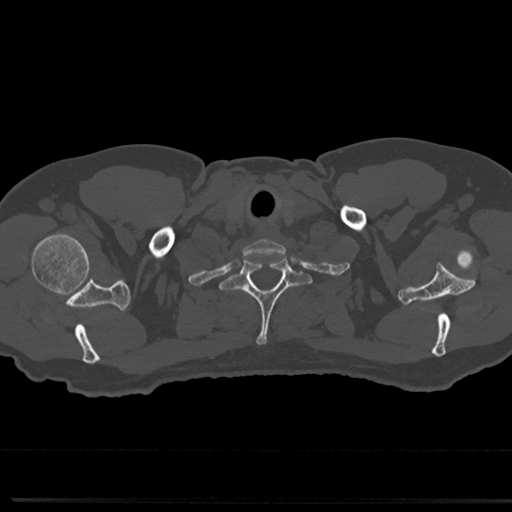
CT including the spine, one axial slice; slice 678 of 817 in the series (ordered by position); reconstruction kernel Br40s/3; 120 kVp; bone window (W 1800 / L 400 HU); 0.5 mm slice thickness; 512 × 512 image matrix, field of view 355 × 355 mm. Male patient, age 61 years. Case-level facts recorded for this patient, not image findings: primary cancer: prostate.
Annotated regions visible in this slice (semi-automatic segmentation, software-assisted and operator-edited):
- T1 vertebra: bounding box <227,252,307,346> (left, top, right, bottom; pixels)
- T2 vertebra: <213,294,314,311>